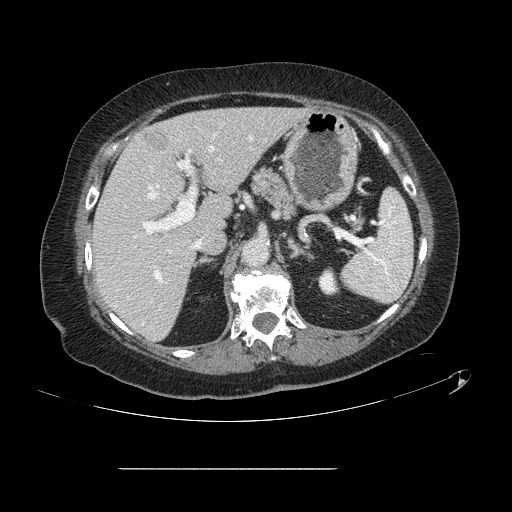
Contrast-enhanced abdominal CT, one axial slice; position 78 of 148 along the scan axis; soft-tissue window (W 400 / L 40 HU); 512 × 512 image matrix, field of view 439 × 439 mm. Female patient, age 75 years. From the clinical record (not read from this slice): diagnosis: colorectal cancer liver metastases, imaged before liver resection; multiple liver metastases: no; largest metastasis: 2.4 cm.
Annotated regions visible in this slice (expert manual segmentation):
- hepatic veins: bounding box (x1, y1, x2, y2) in pixels: (149, 146, 214, 248)
- liver: (93, 108, 302, 340)
- planned liver remnant (the part of the liver to remain after resection): (93, 108, 302, 340)
- portal vein (with intrahepatic branches): (132, 134, 253, 282)
- liver metastasis: (144, 129, 170, 154)